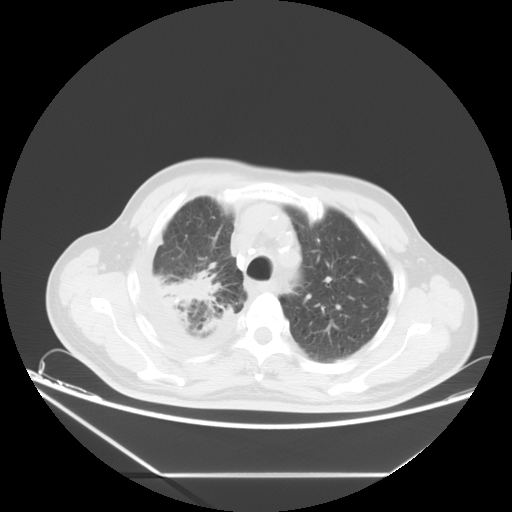
Chest CT, one axial slice. Position 12 of 16 along the scan axis. Reconstruction kernel STANDARD. 120 kVp. Lung window (W 1500 / L -600 HU). 5 mm slice thickness. 512 × 512 image matrix, field of view 418 × 418 mm. Patient: male, 75 years. Case-level facts recorded for this patient, not image findings: clinical TNM (as recorded): T1c N1 M1.
Annotated regions visible in this slice (rectangle marked by the reading radiologist):
- lung tumour (recorded histology: adenocarcinoma): box from (x=150, y=260) to (x=215, y=309) px